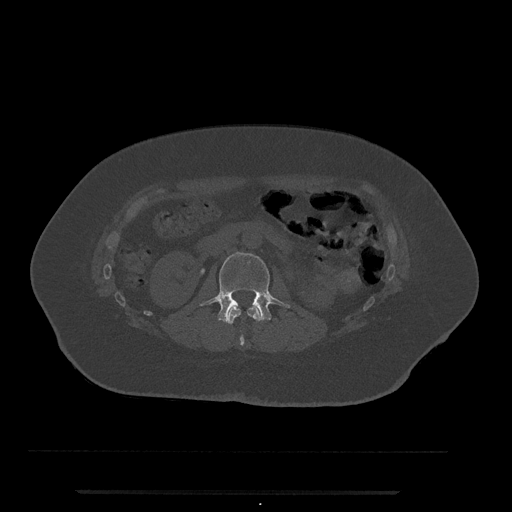
CT including the spine, one axial slice; reconstruction kernel Br40s/3; 120 kVp; bone window (W 1800 / L 400 HU); 512 × 512 image matrix, field of view 440 × 440 mm. Female patient, age 51 years. Case-level facts recorded for this patient, not image findings: primary cancer: neuro; vertebrae with lytic lesions (as recorded): T8.
Annotated regions visible in this slice (semi-automatic segmentation, software-assisted and operator-edited):
- L1 vertebra: box from (x=225, y=306) to (x=262, y=346) px
- L2 vertebra: (x=201, y=252)–(x=290, y=323)